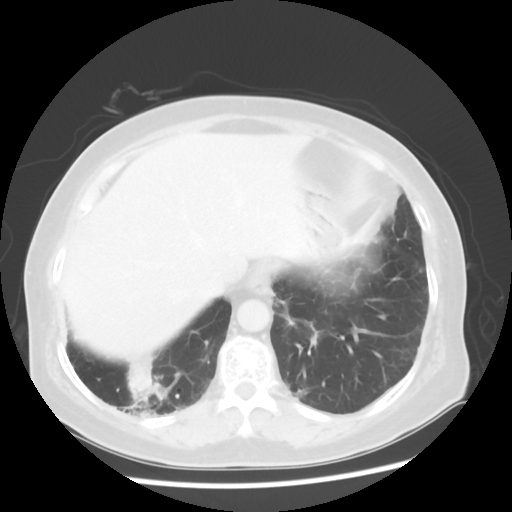
Chest CT, one axial slice; position 13 of 56 along the scan axis; lung window (W 1500 / L -600 HU); 512 × 512 image matrix. Patient: female, 64 years. Case-level facts recorded for this patient, not image findings: clinical TNM (as recorded): Tis N0 M0.
Structures marked on this image (bounding box drawn by a radiologist):
- lung tumour (recorded histology: adenocarcinoma): box from (x=118, y=353) to (x=181, y=429) px